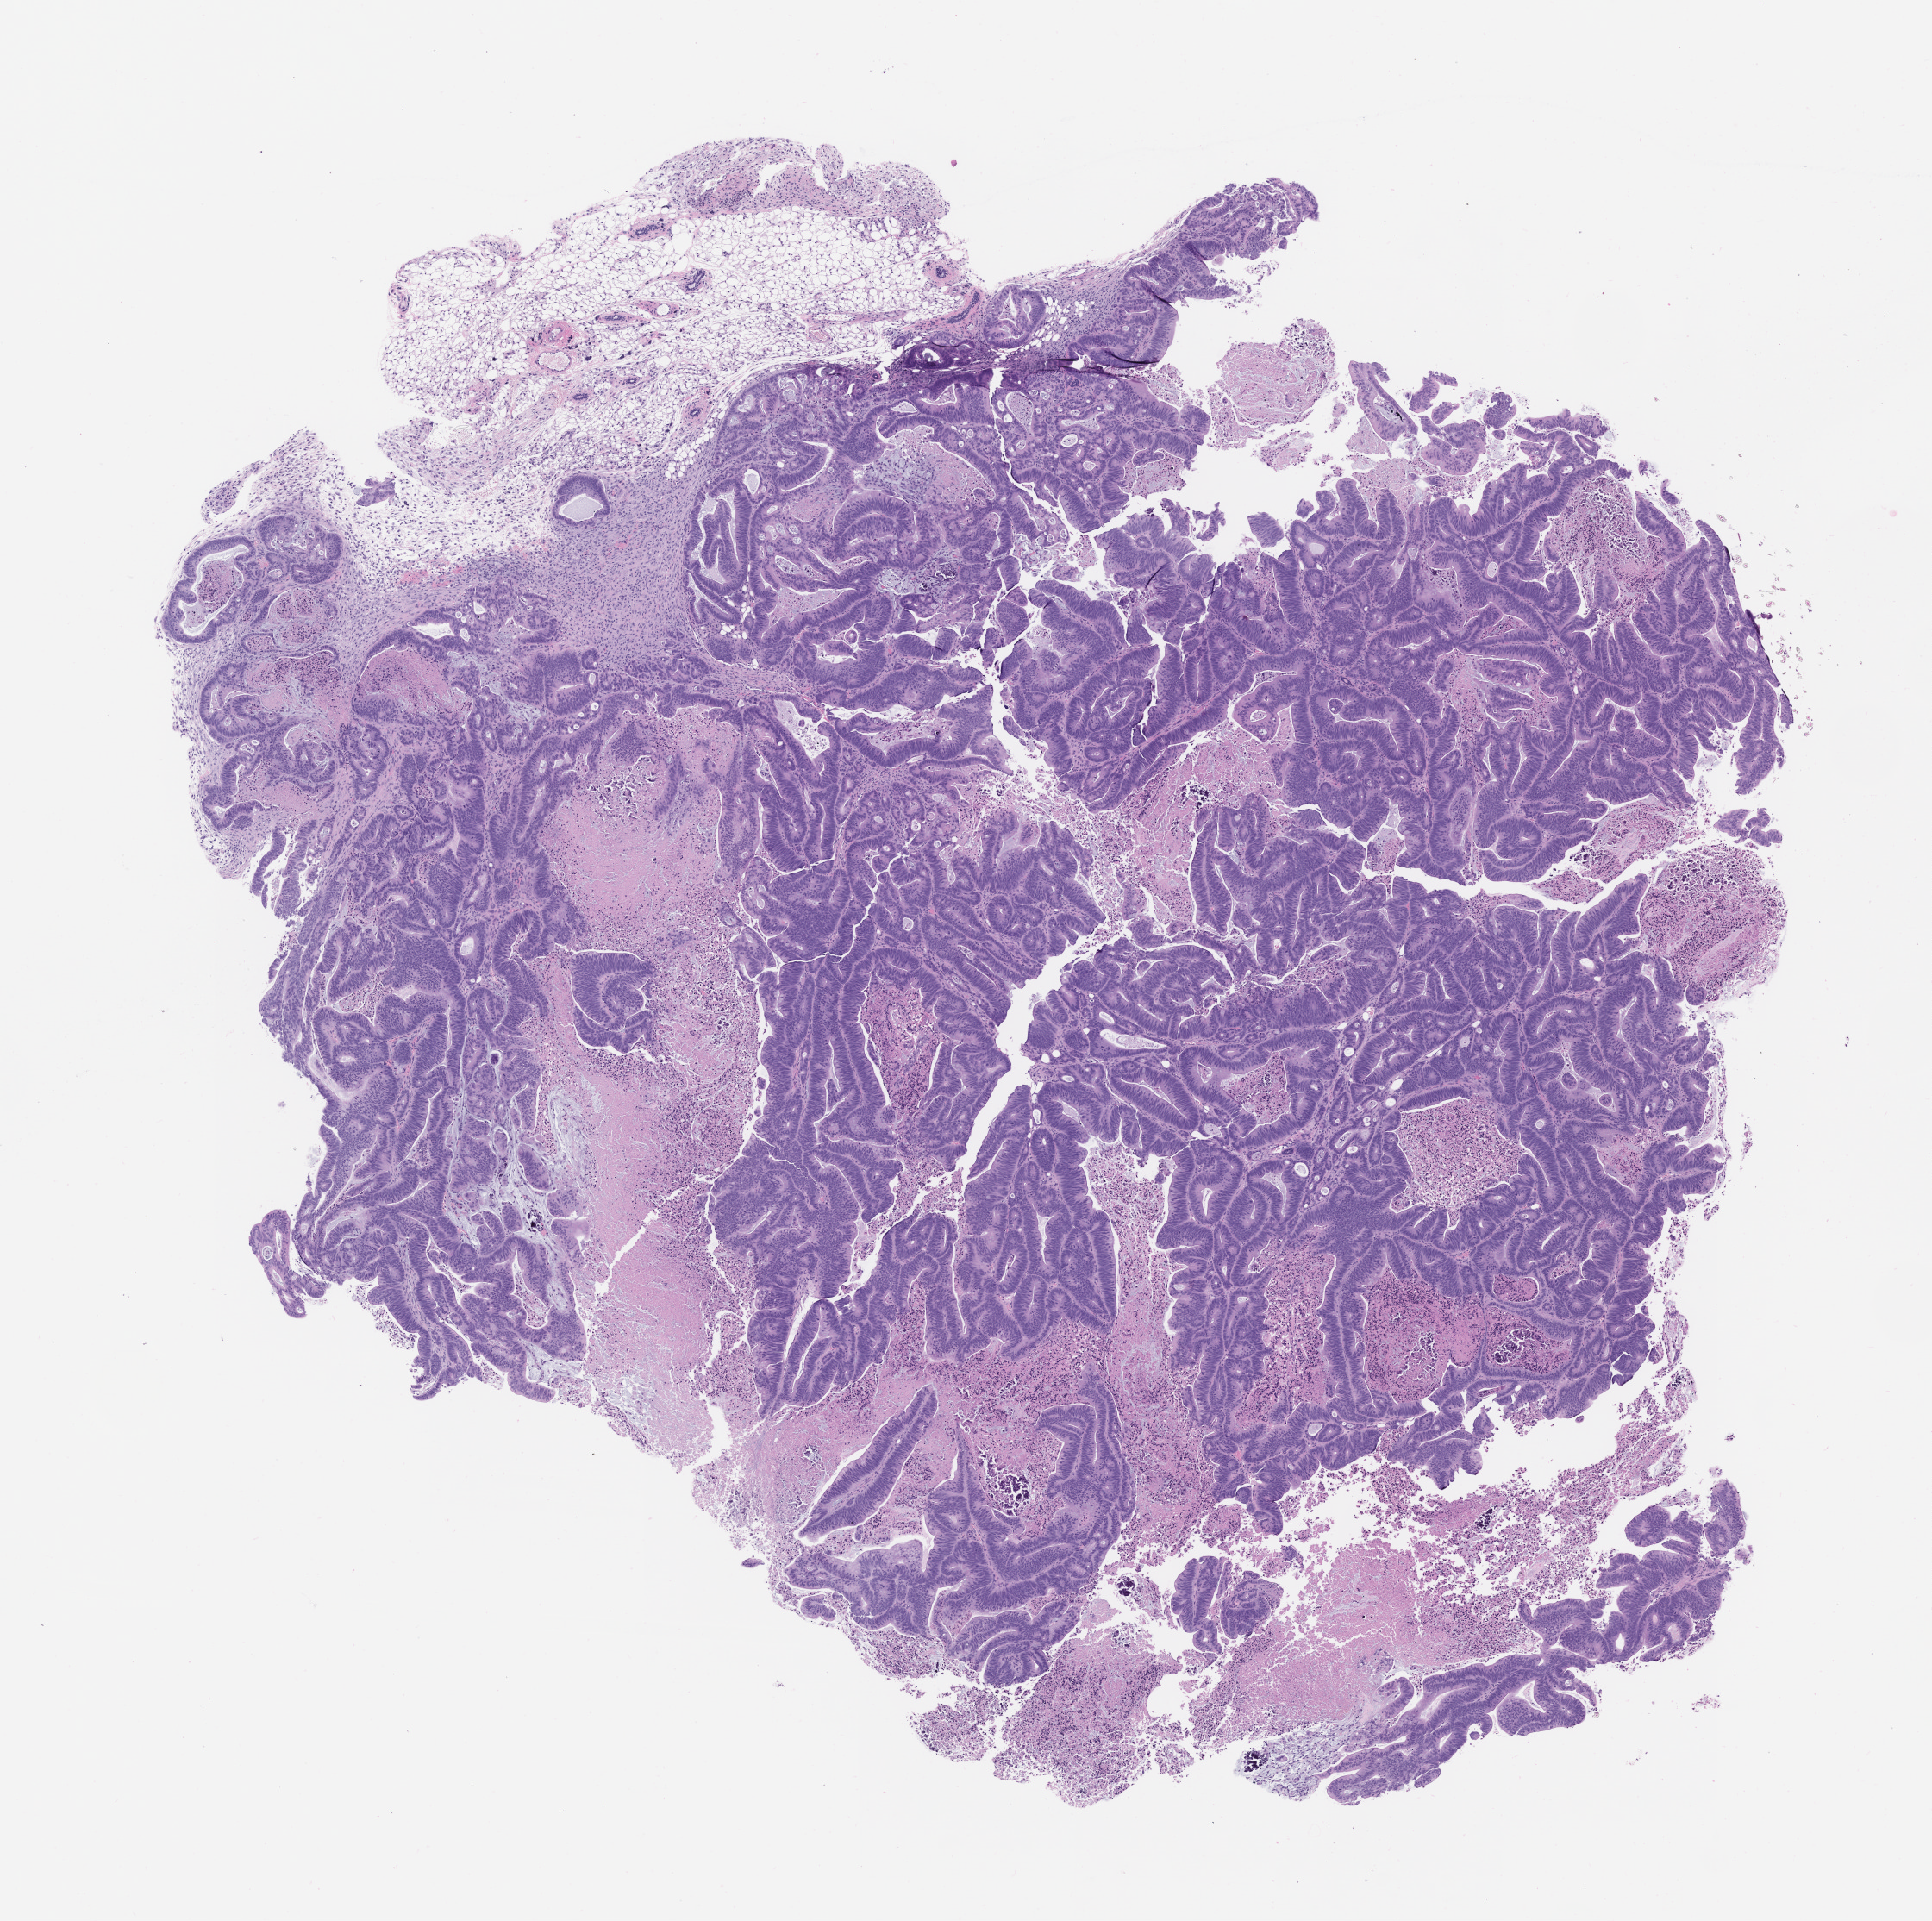
H&E whole-slide image of a patient-derived xenograft (PDX) tumor grown in a mouse, passage 2 — low-resolution overview of the scanned area, about 9.0 x 9.0 mm; formalin-fixed paraffin-embedded section; originating tumor site category: colon.
* originating patient diagnosis: Colon Adenocarcinoma